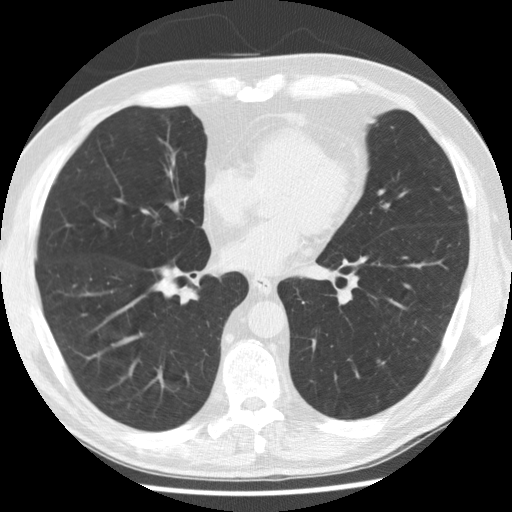
Low-dose screening chest CT, axial slice. Baseline annual screen. Lung window (W 1500 / L -600 HU). 2.5 mm slice thickness. Slice 150 of 265 in the series. Male participant, aged 58 years at enrolment. Former smoker at enrolment.
• Expert reader's lesion annotation, bounding box <366,346,398,377> (left, top, right, bottom; pixels).
• Screening reader's record for this exam: no non-calcified nodule ≥4 mm recorded.
• Official screen result: negative screen, no significant abnormalities.